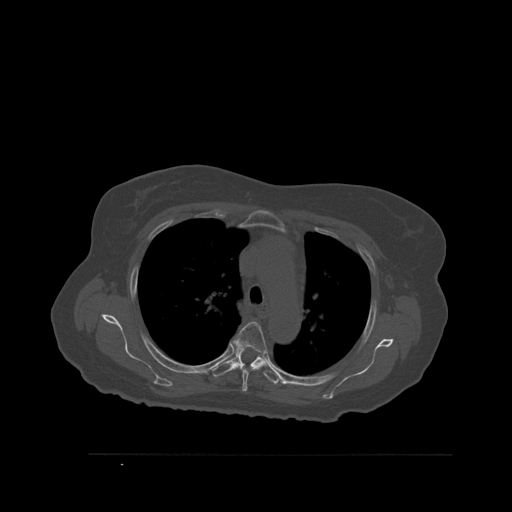
CT including the spine, one axial slice; position 402 of 527 along the scan axis; bone window (W 1800 / L 400 HU); 512 × 512 image matrix, field of view 470 × 470 mm. Patient: female, 73 years. From the clinical record (not read from this slice): primary cancer: breast.
Annotated regions visible in this slice (semi-automatically segmented with operator editing):
- T4 vertebra: box from (x=234, y=322) to (x=267, y=392) px
- T5 vertebra: (x=211, y=342)–(x=279, y=385)